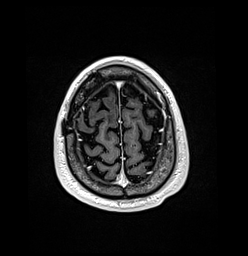
Brain MRI from a brain-tumour surgery series, one axial slice. Slice 26 of 176 in the series (ordered by position). T1-weighted post-contrast. 1 mm slice thickness. 248 × 256 image matrix. Case-level facts recorded for this patient, not image findings: histopathology: Oligodendroglioma; WHO grade: 3; IDH mutation: yes; tumour location: Right Frontal.
Structures marked on this image (manually delineated by an expert):
- previous resection cavity: box from (x=76, y=111) to (x=81, y=119) px